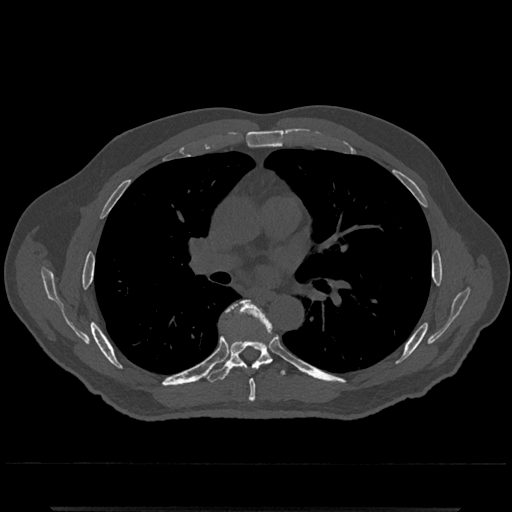
CT including the spine, one axial slice; position 744 of 797 along the scan axis; 120 kVp; bone window (W 1800 / L 400 HU); 0.5 mm slice thickness; 512 × 512 image matrix. Patient: male, 67 years. Case-level facts recorded for this patient, not image findings: primary cancer: prostate.
Outlined on this slice (semi-automatically segmented with operator editing):
- T6 vertebra: bounding box (x1, y1, x2, y2) in pixels: (227, 300, 265, 402)
- T7 vertebra: (205, 305, 290, 385)